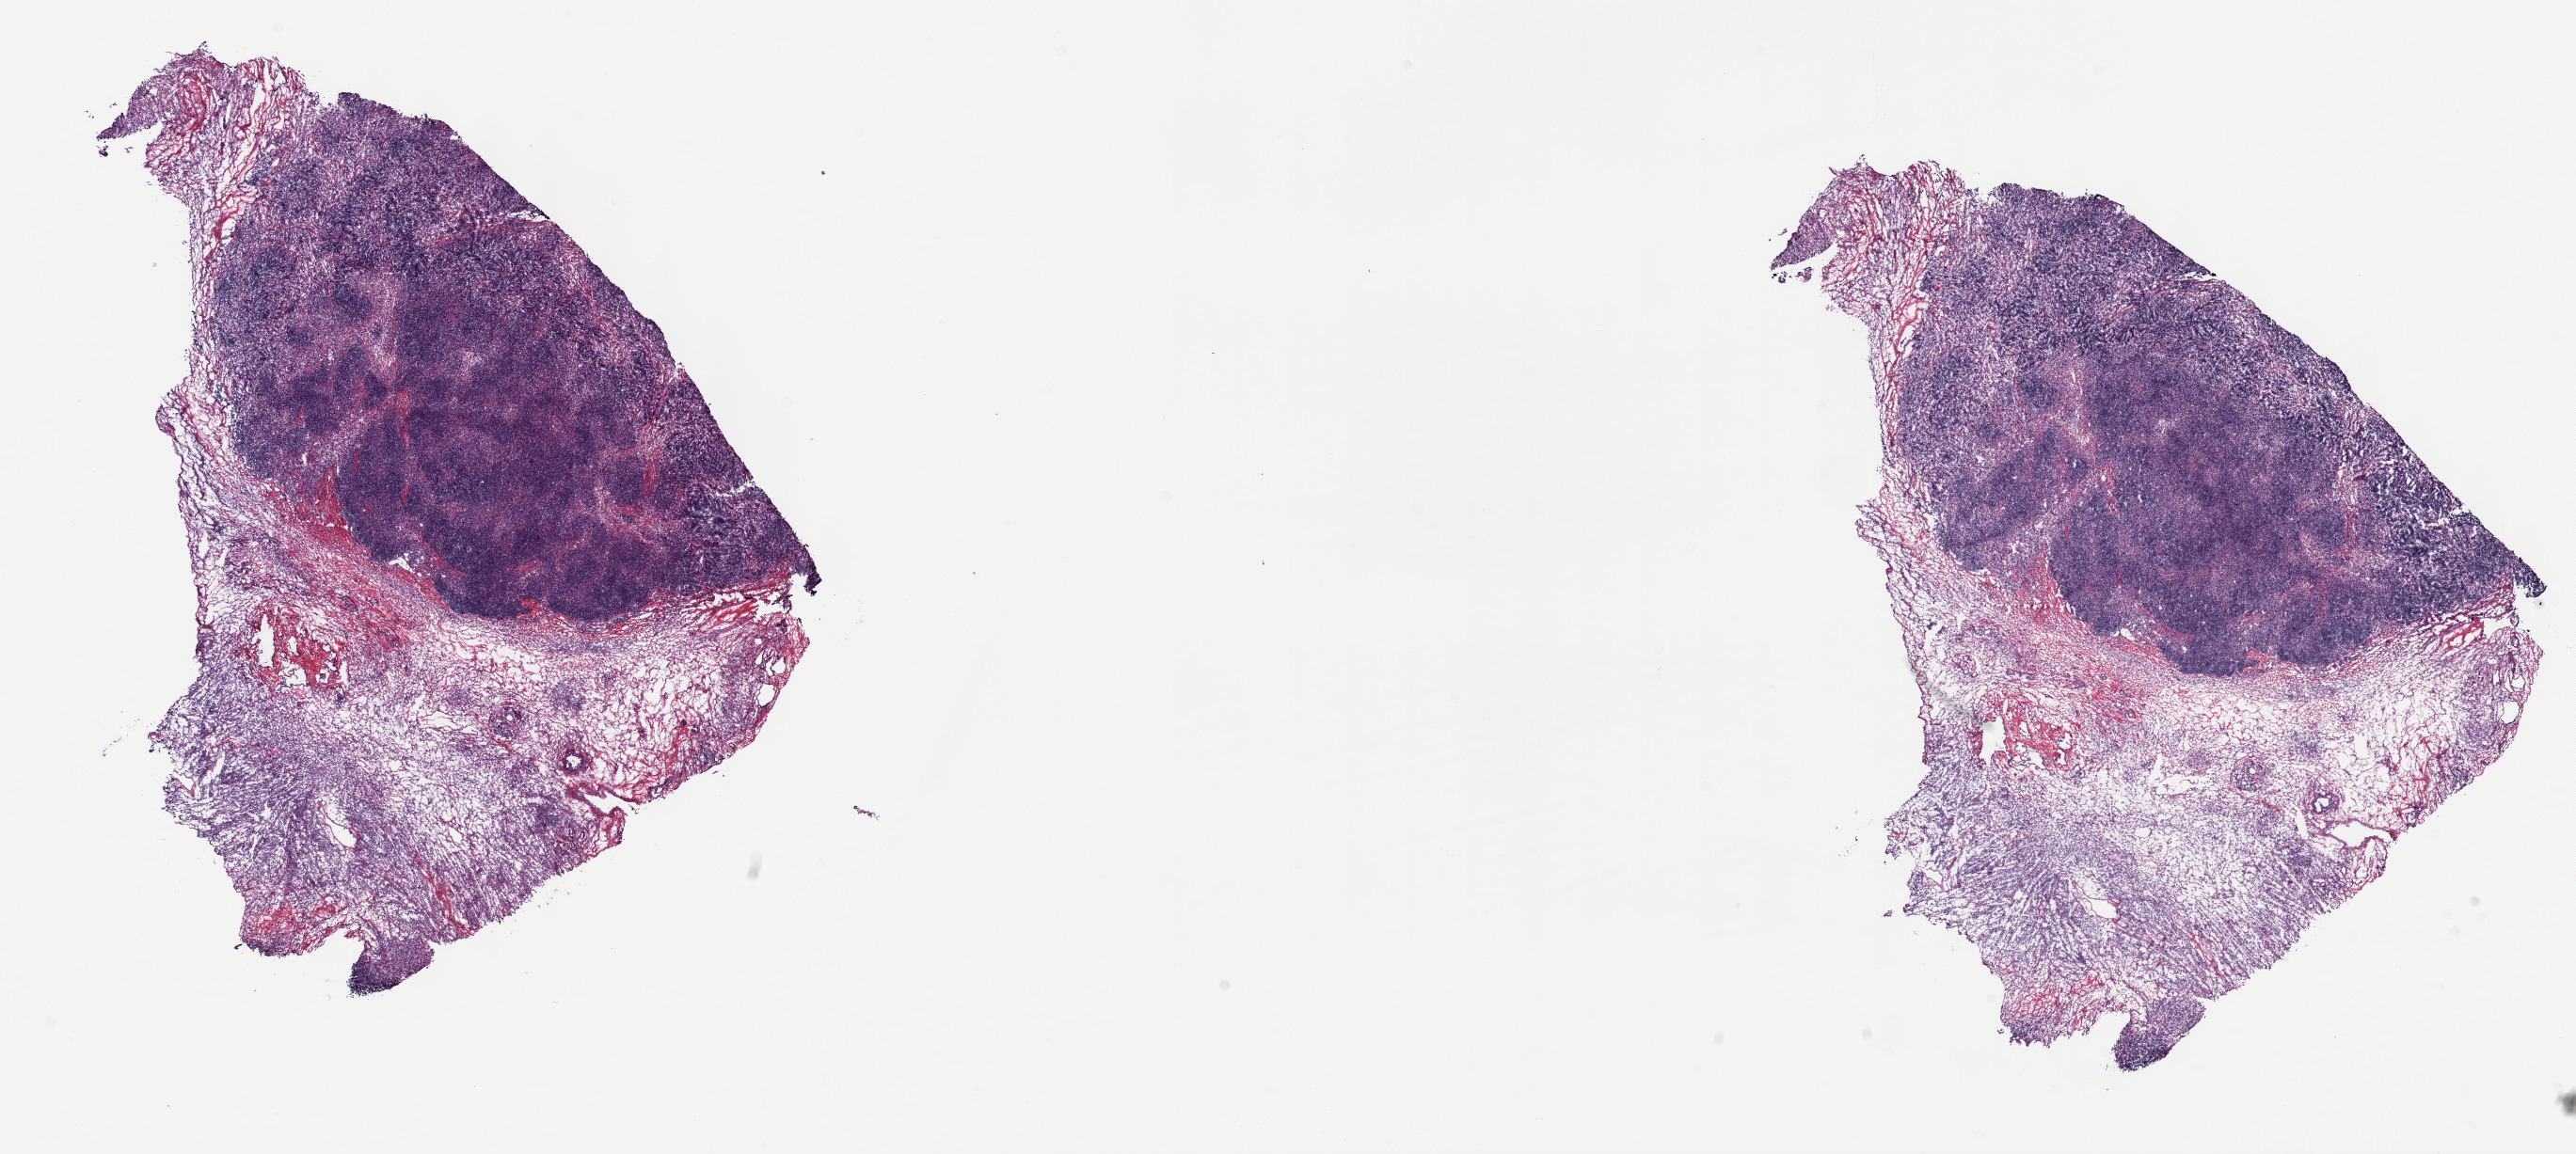
Hematoxylin and eosin (H&E) stained whole-slide image — shown as a low-resolution overview of the whole scanned area (about 22.1 x 9.9 mm). Frozen section from the top of the tissue portion. Primary tumour sample from the thymus. Female, age 56 years at initial diagnosis. Slide review estimates, as recorded: tumour cells 100%, tumour nuclei 75%, normal cells 0%, stromal cells 0%, necrosis 0%. Infiltration values recorded for this section: lymphocyte infiltration 2%, monocyte infiltration 0%, neutrophil infiltration 0%.
- histologic diagnosis: Thymoma, type AB, malignant (anterior mediastinum)